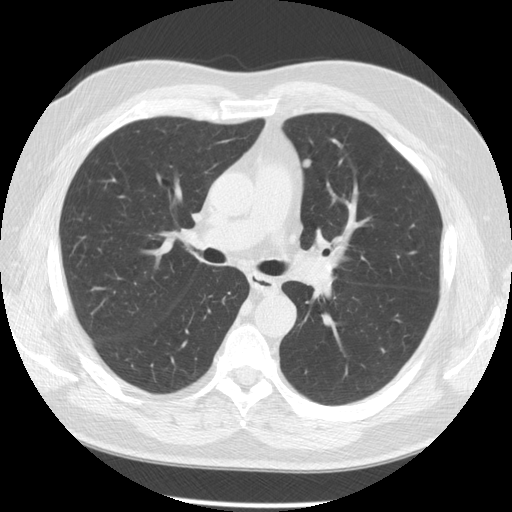
Low-dose screening chest CT, one axial slice. Position 85 of 137 along the scan axis. Reconstruction kernel STANDARD. Lung window (W 1500 / L -600 HU). 2.5 mm slice thickness. 512 × 512 image matrix, field of view 370 × 370 mm.
Annotated regions visible in this slice (expert manual segmentation):
- lesion 1 (tumor, upper lobe of left lung): bounding box <303,159,311,168> (left, top, right, bottom; pixels)